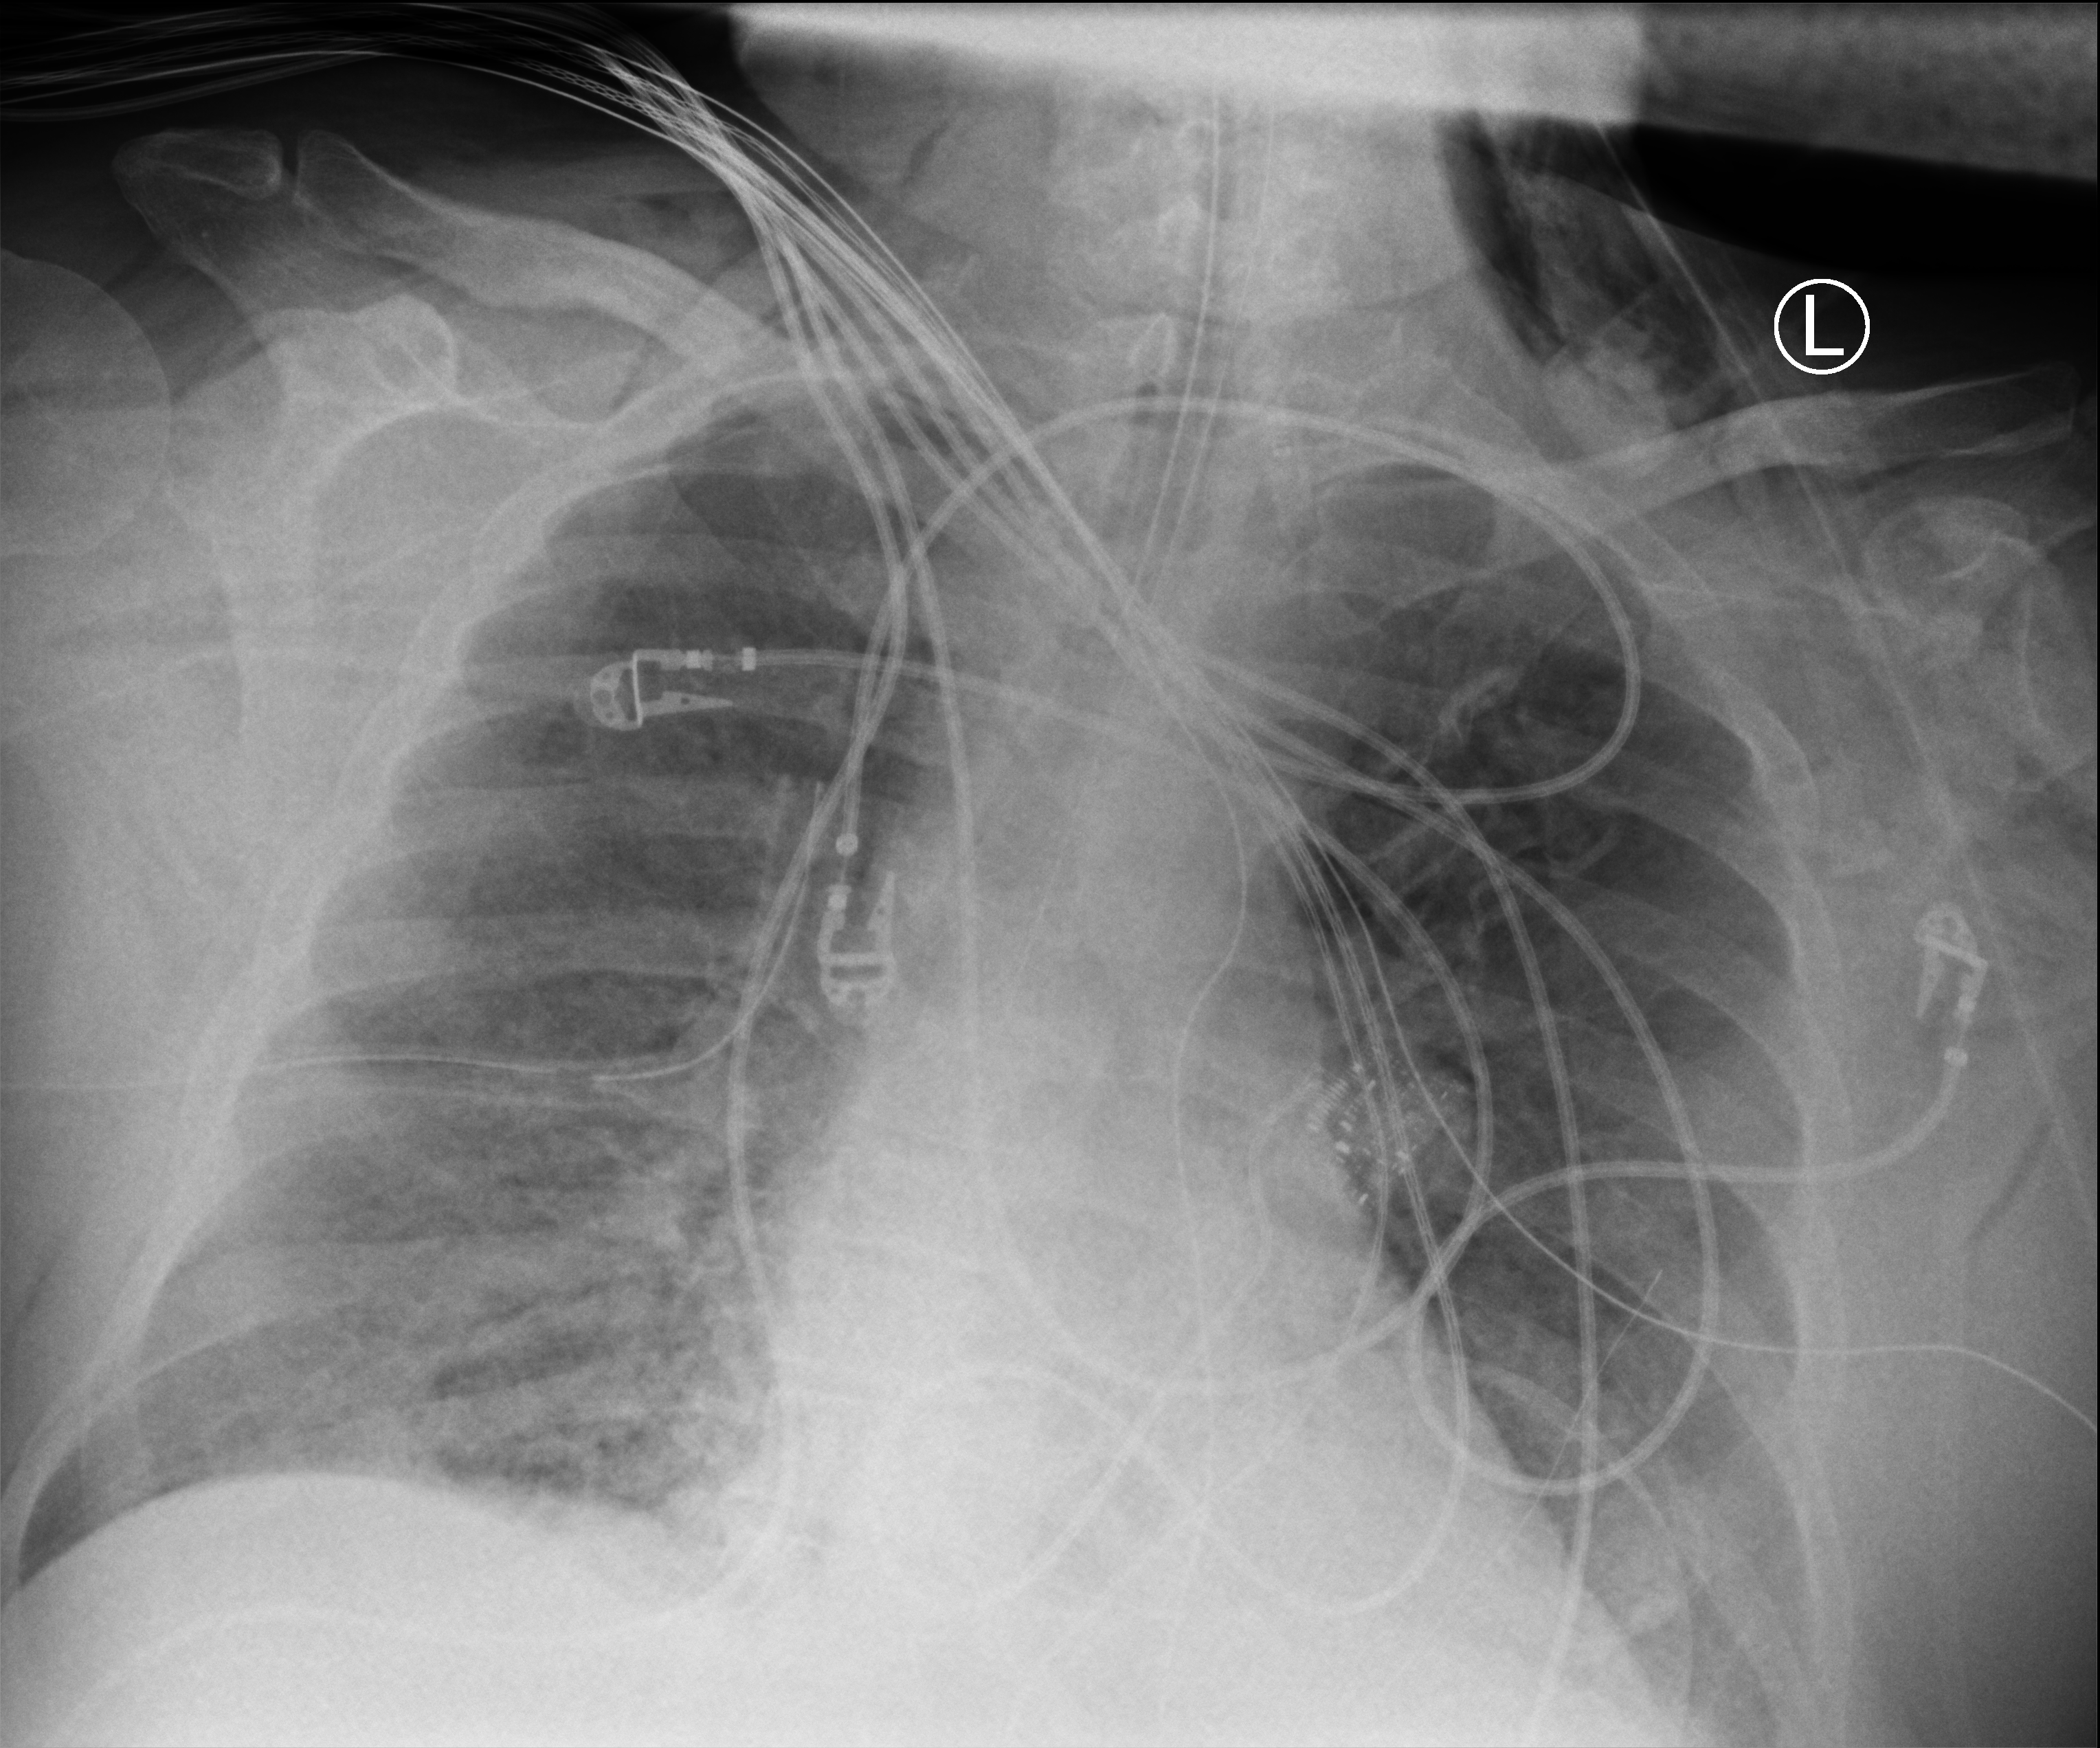
Portable chest radiograph; anteroposterior (AP) projection. Patient hospitalised with COVID-19, aged 18–59 years.
Admission-level facts for this patient (not findings on this image; timing relative to this image not recorded):
- mechanically ventilated during this hospital stay: yes